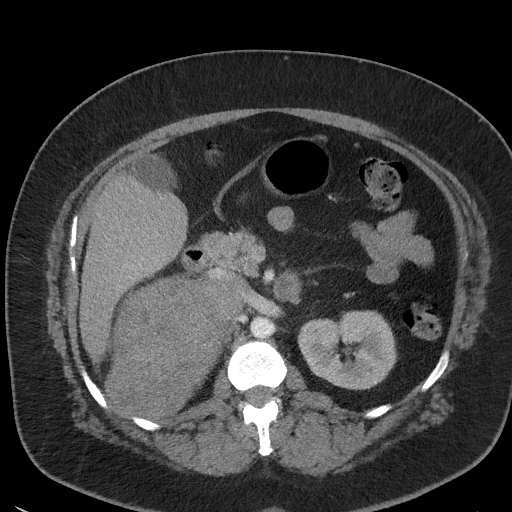
Contrast-enhanced abdominal CT, one axial slice; slice 26 of 56 in the series (ordered by position); reconstruction kernel I41f/3; intravenous contrast given; soft-tissue window (W 400 / L 40 HU); 512 × 512 image matrix, field of view 373 × 373 mm. Patient: female, 35 years. From the clinical record (not read from this slice): diagnosis: adrenocortical carcinoma; tumour side: right adrenal.
Annotated regions visible in this slice (semi-automatically segmented with operator editing):
- mass: bounding box (x1, y1, x2, y2) in pixels: (110, 280, 236, 414)